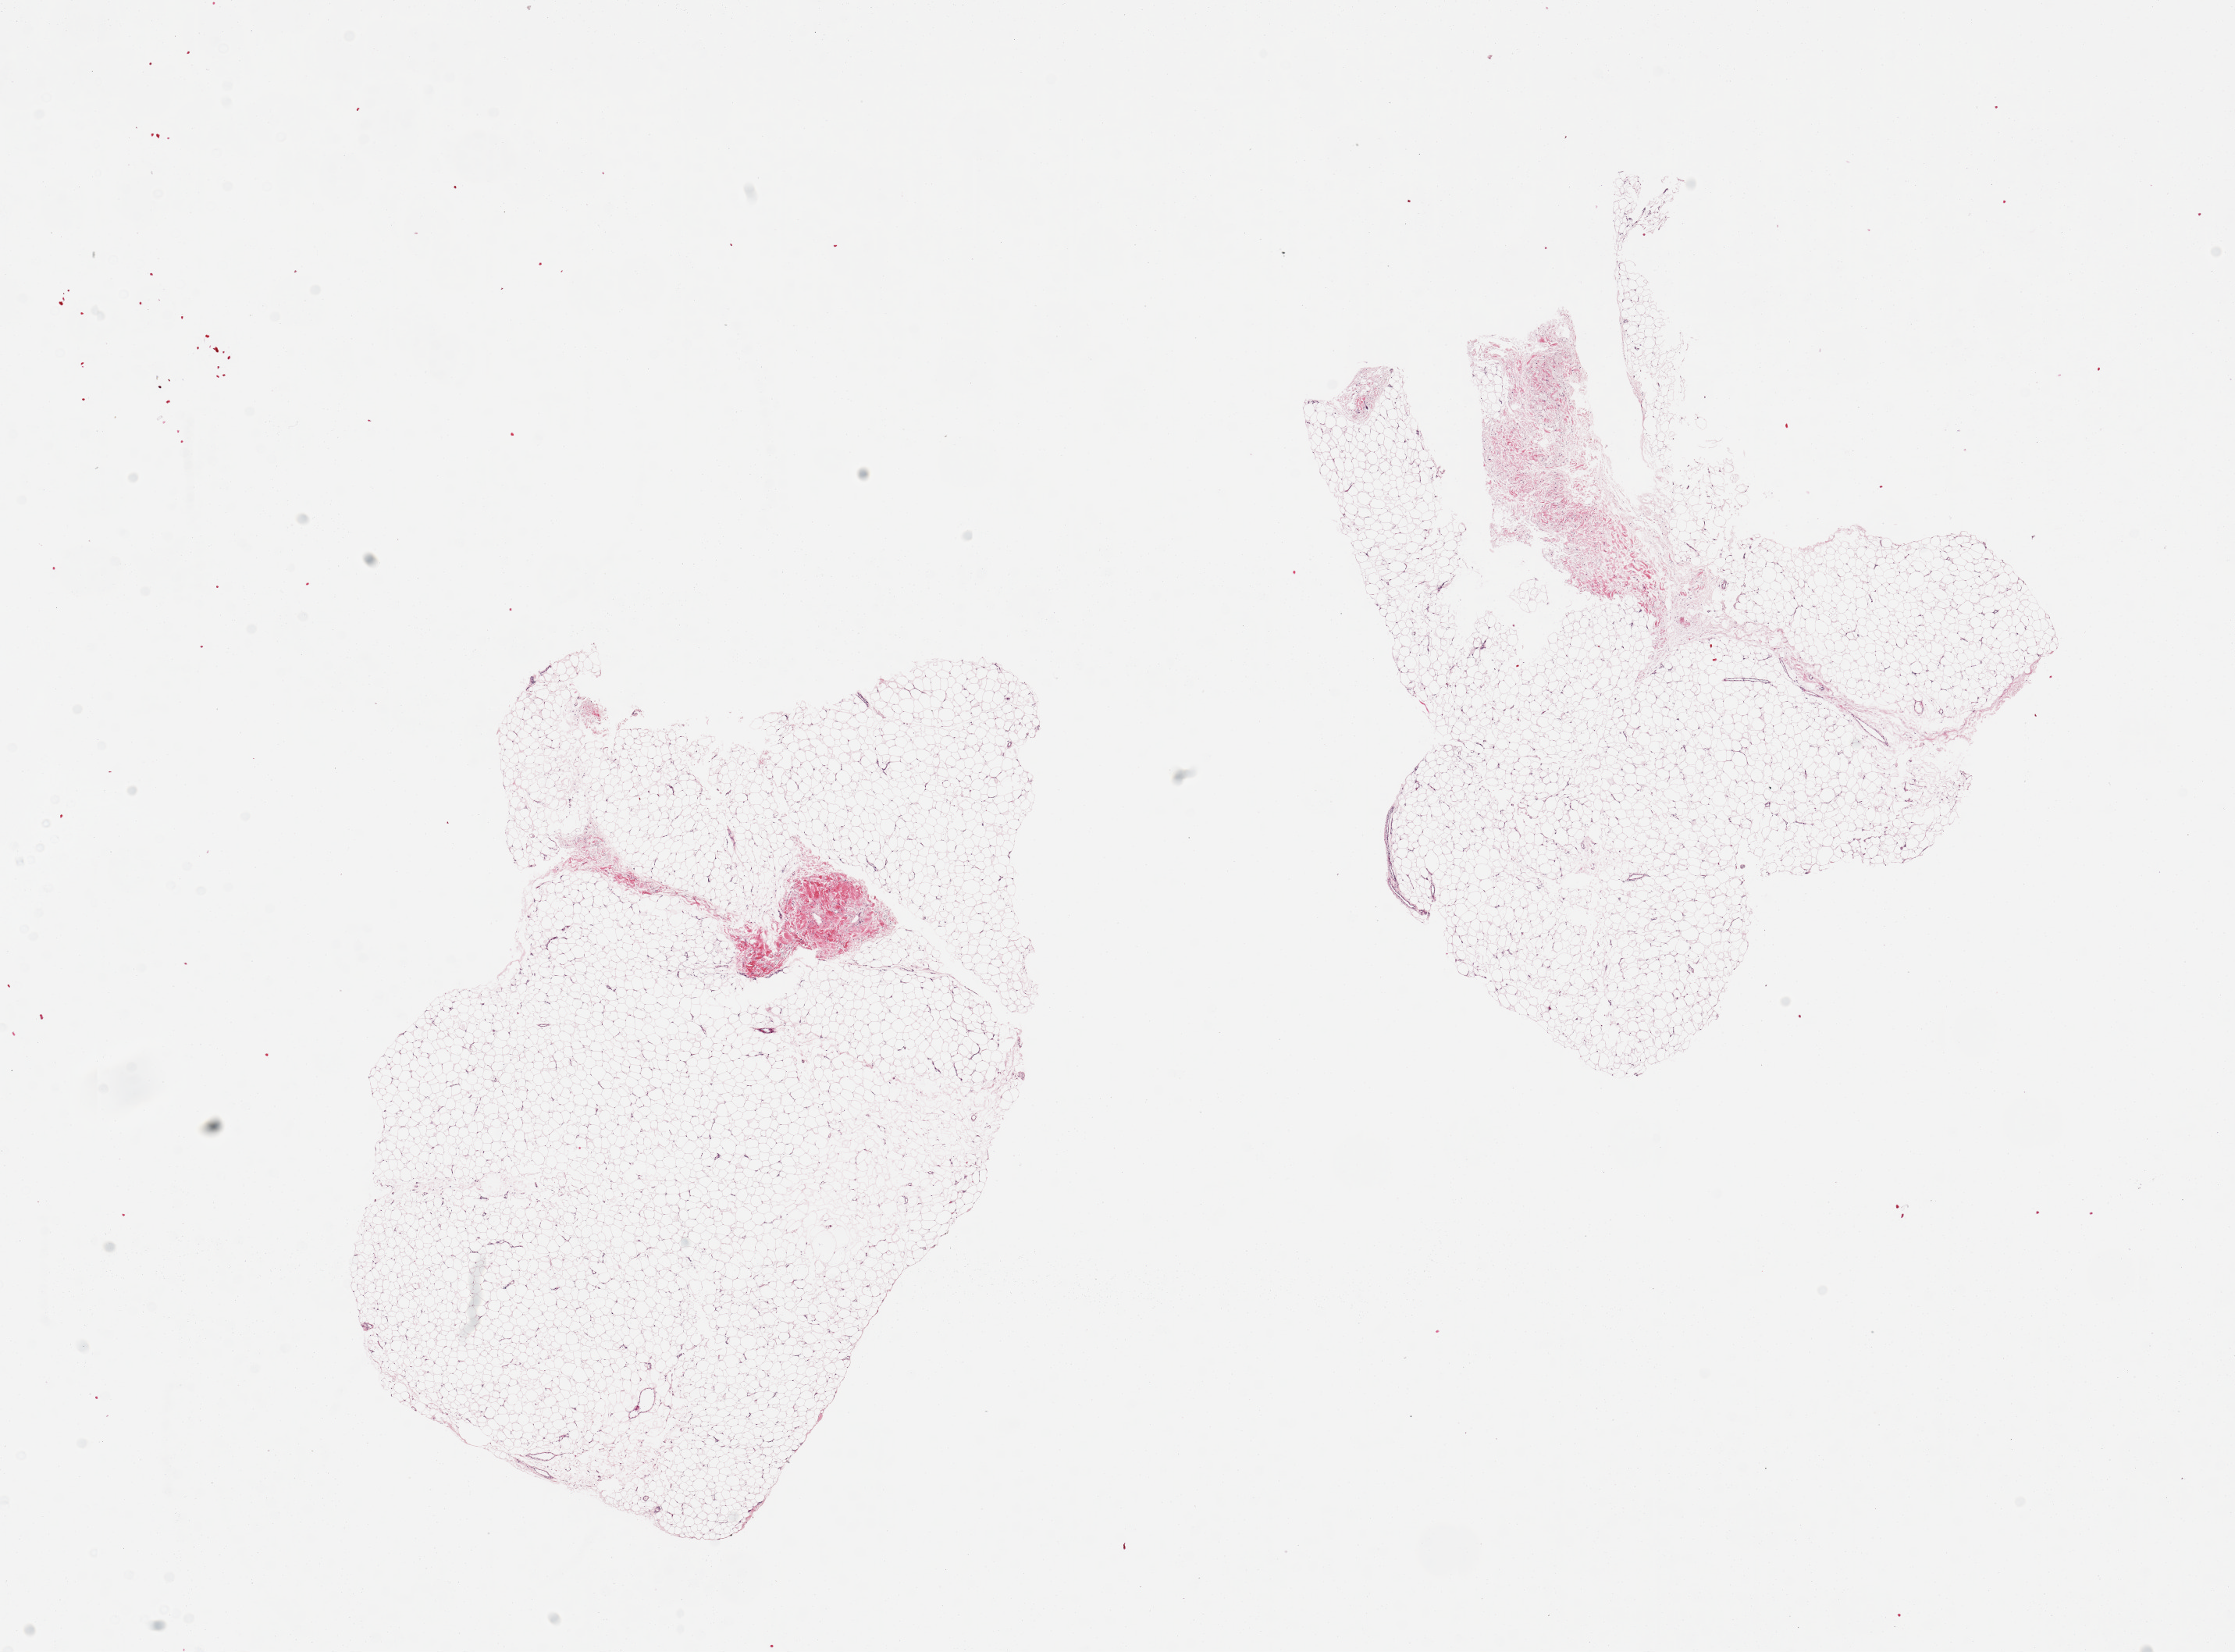
Digitized H&E-stained section — whole scanned area (about 22.6 x 16.7 mm) shown as a low-resolution overview, PAXgene-fixed paraffin-embedded (PFPE) section, sampled site (target tissue): adipose tissue, donor tissue sample. Donor: female.
Reviewer comment on this tissue sample: 2 pieces, <10% is fibrous.